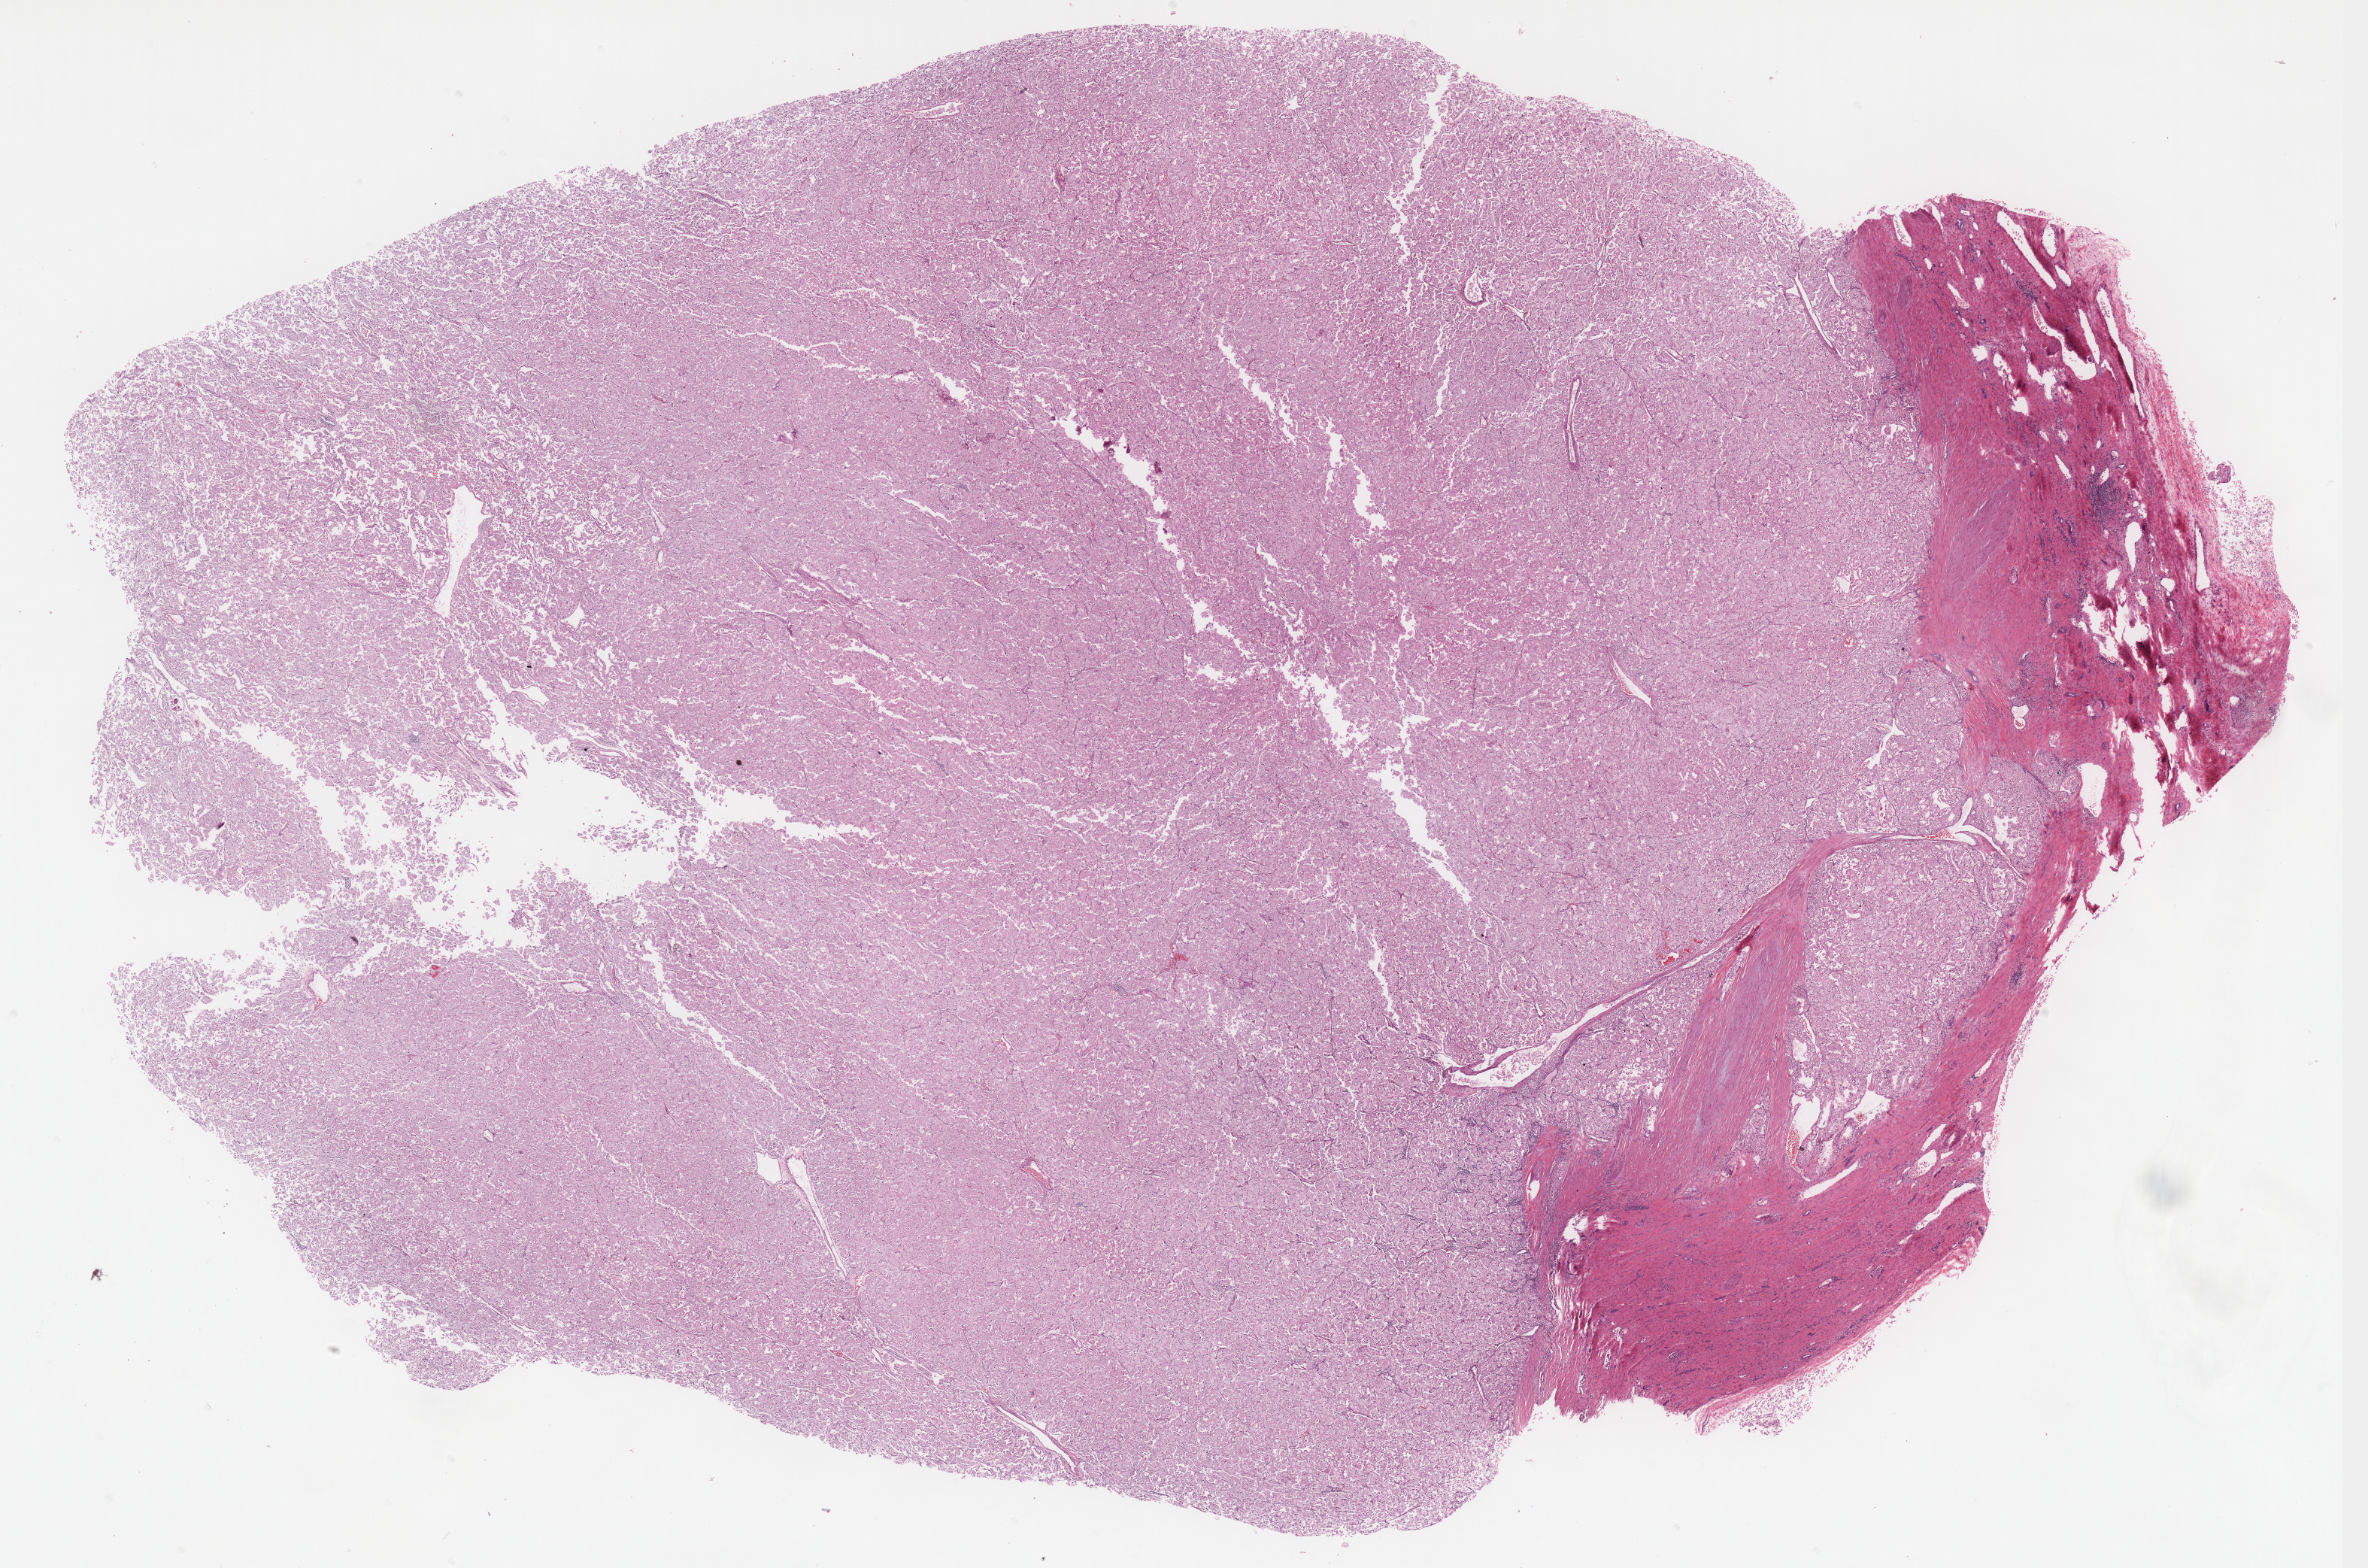
Whole-slide histology image, H&E, shown as a low-resolution overview of the whole scanned area (about 25.2 x 16.7 mm, acquisition: 40x scan). Formalin-fixed paraffin-embedded (FFPE) diagnostic section. Primary tumour sample from the kidney. Female, age 45 years at initial diagnosis.
• AJCC pathologic stage: II
• lymph nodes positive (case pathology): 0 of 9 examined
• laterality: left
• histologic diagnosis: Renal cell carcinoma, chromophobe type